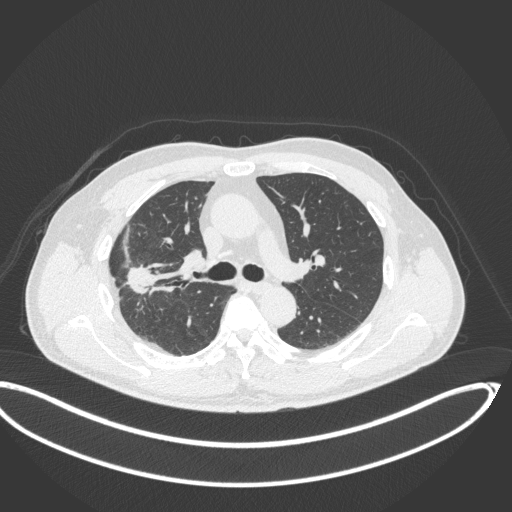
Chest CT, one axial slice. Slice 220 of 341 in the series (ordered by position). Reconstruction kernel B31f. 120 kVp. Lung window (W 1500 / L -600 HU). 1 mm slice thickness. 512 × 512 image matrix, field of view 439 × 439 mm. Patient: male, 63 years. From the clinical record (not read from this slice): clinical TNM (as recorded): T1c N0 M0.
Structures marked on this image (rectangle marked by the reading radiologist):
- lung tumour (recorded histology: adenocarcinoma): bounding box [x1, y1, x2, y2] px = [119, 256, 160, 303]